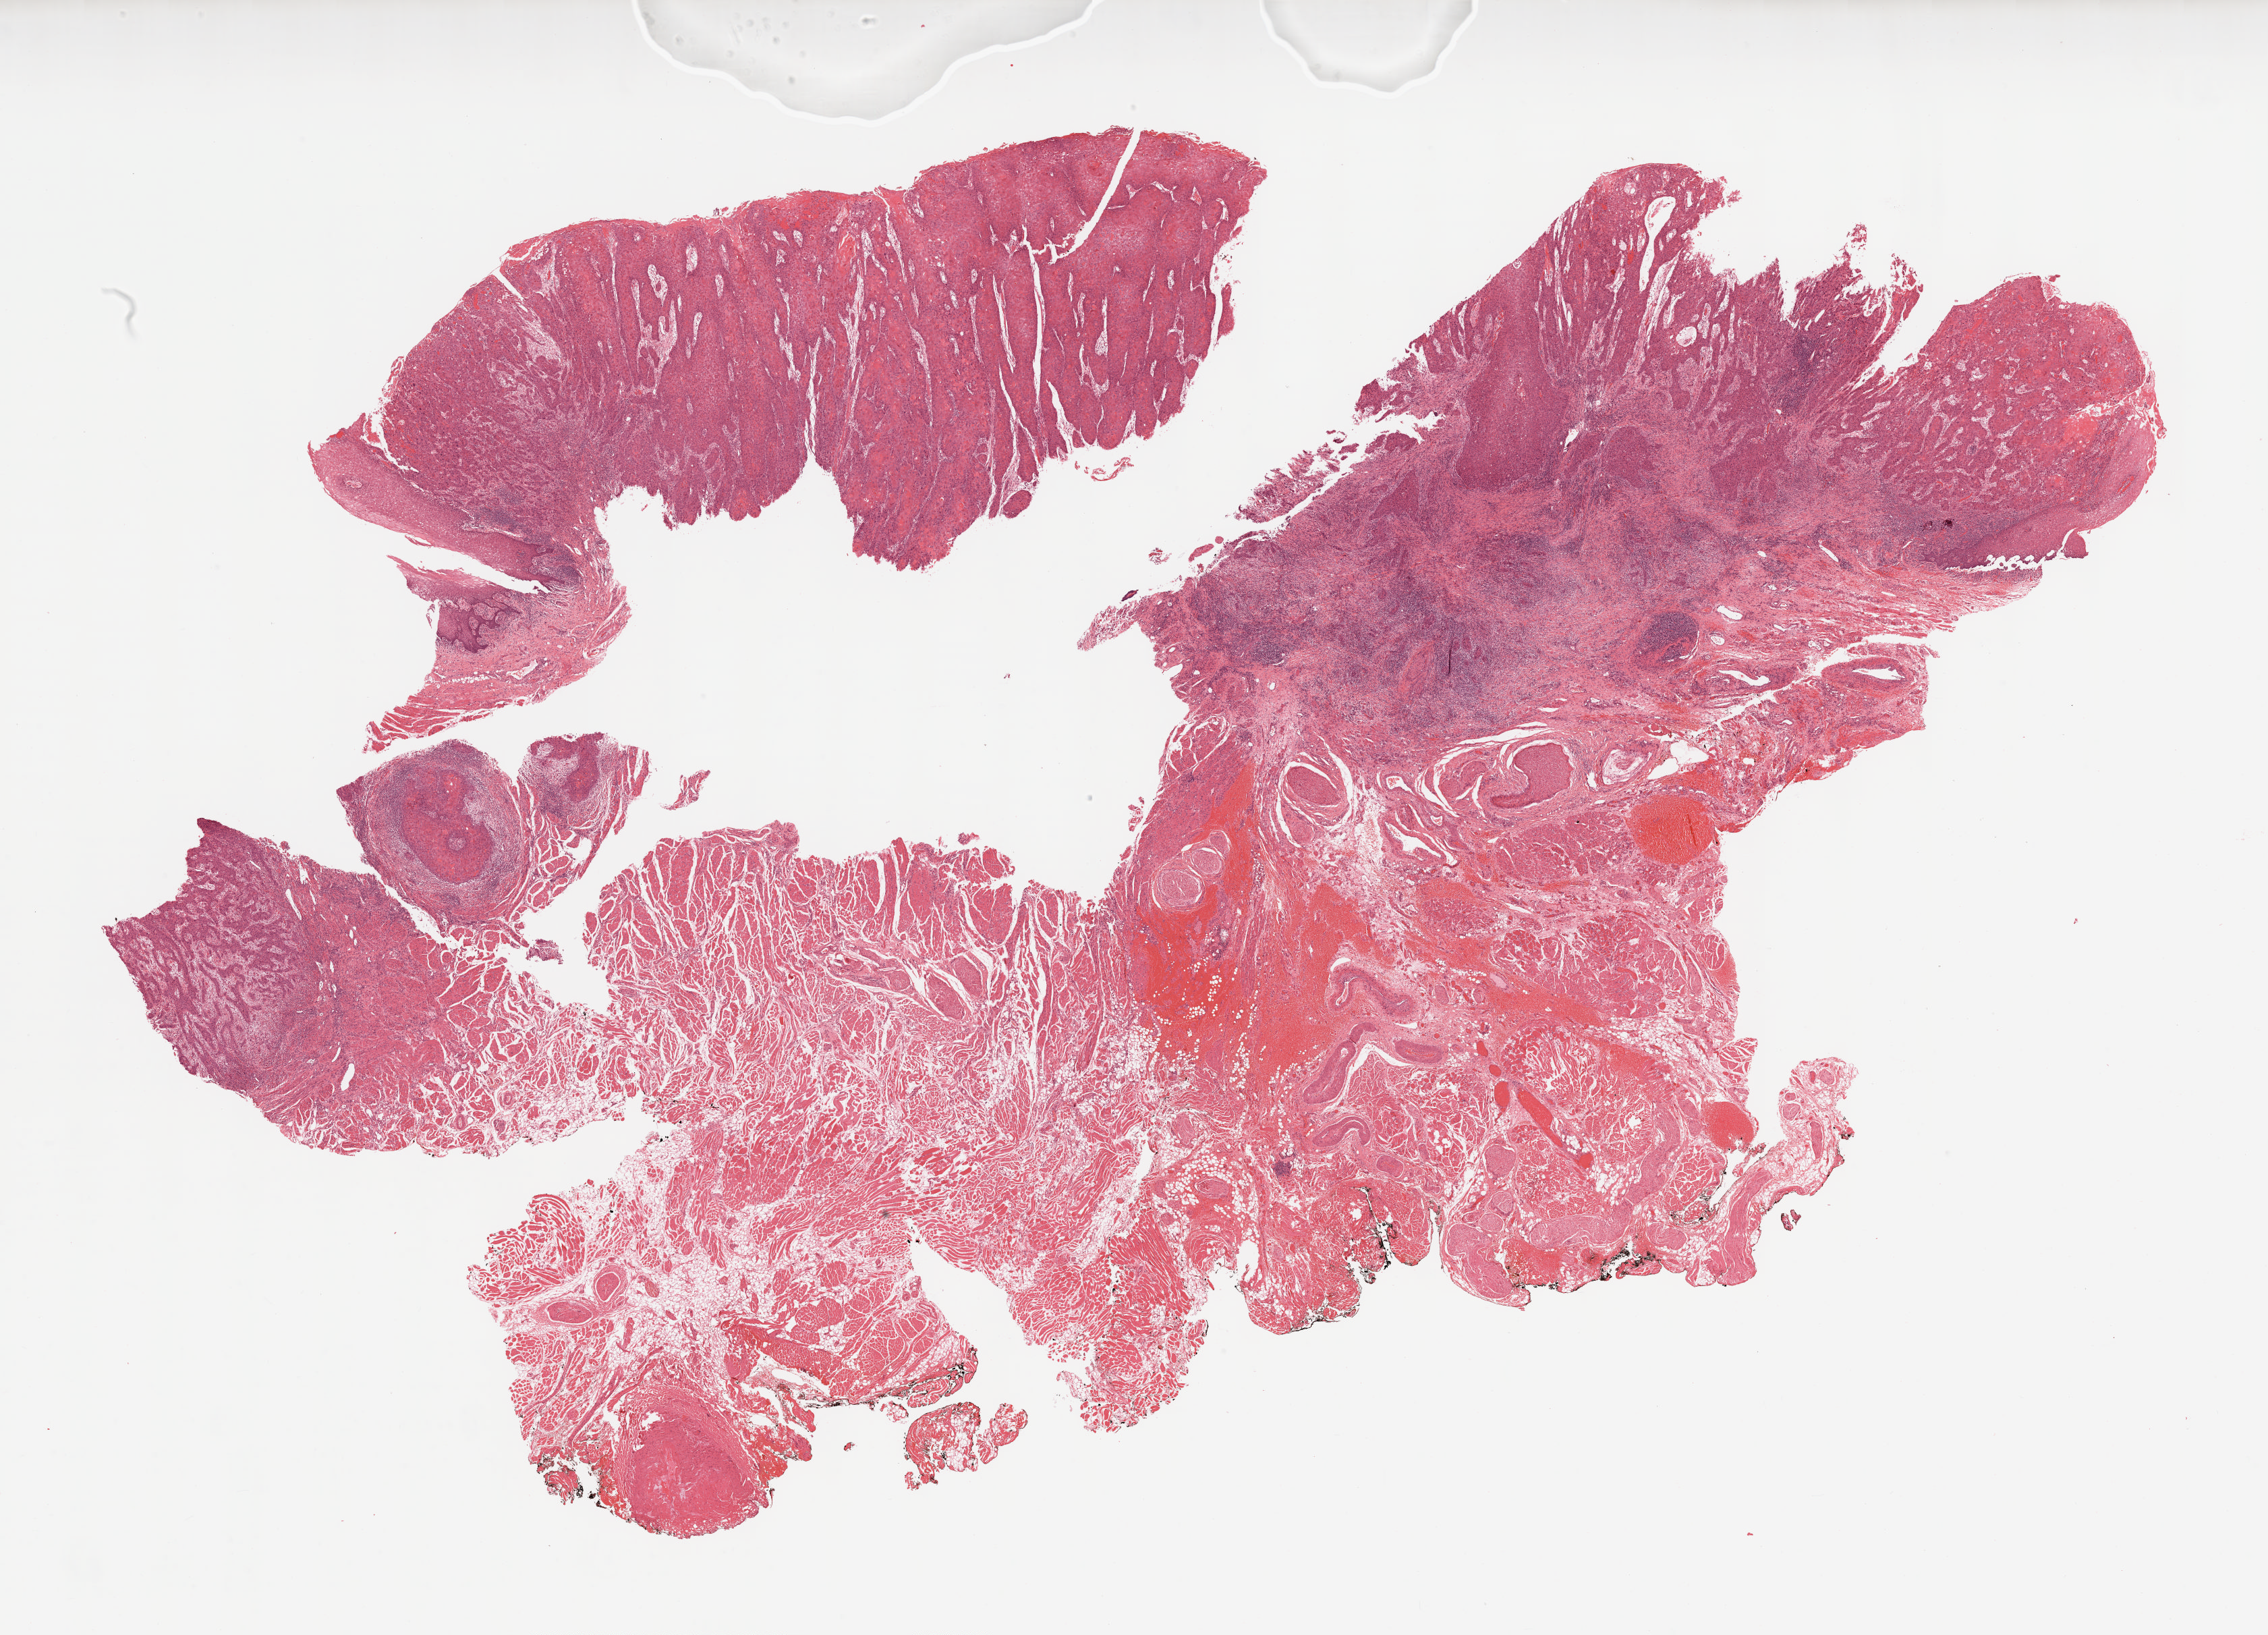
Whole-slide histology image, H&E — shown as a low-resolution overview of the whole scanned area (about 27.0 x 19.4 mm); formalin-fixed paraffin-embedded (FFPE) diagnostic section; sample: primary tumour, head and neck. Patient sex: male. Histologic grade: G2 (moderately differentiated).
Laterality: left. AJCC pathologic stage: II (7th edition). Pathologic diagnosis: Squamous cell carcinoma, NOS (ventral surface of tongue, NOS).